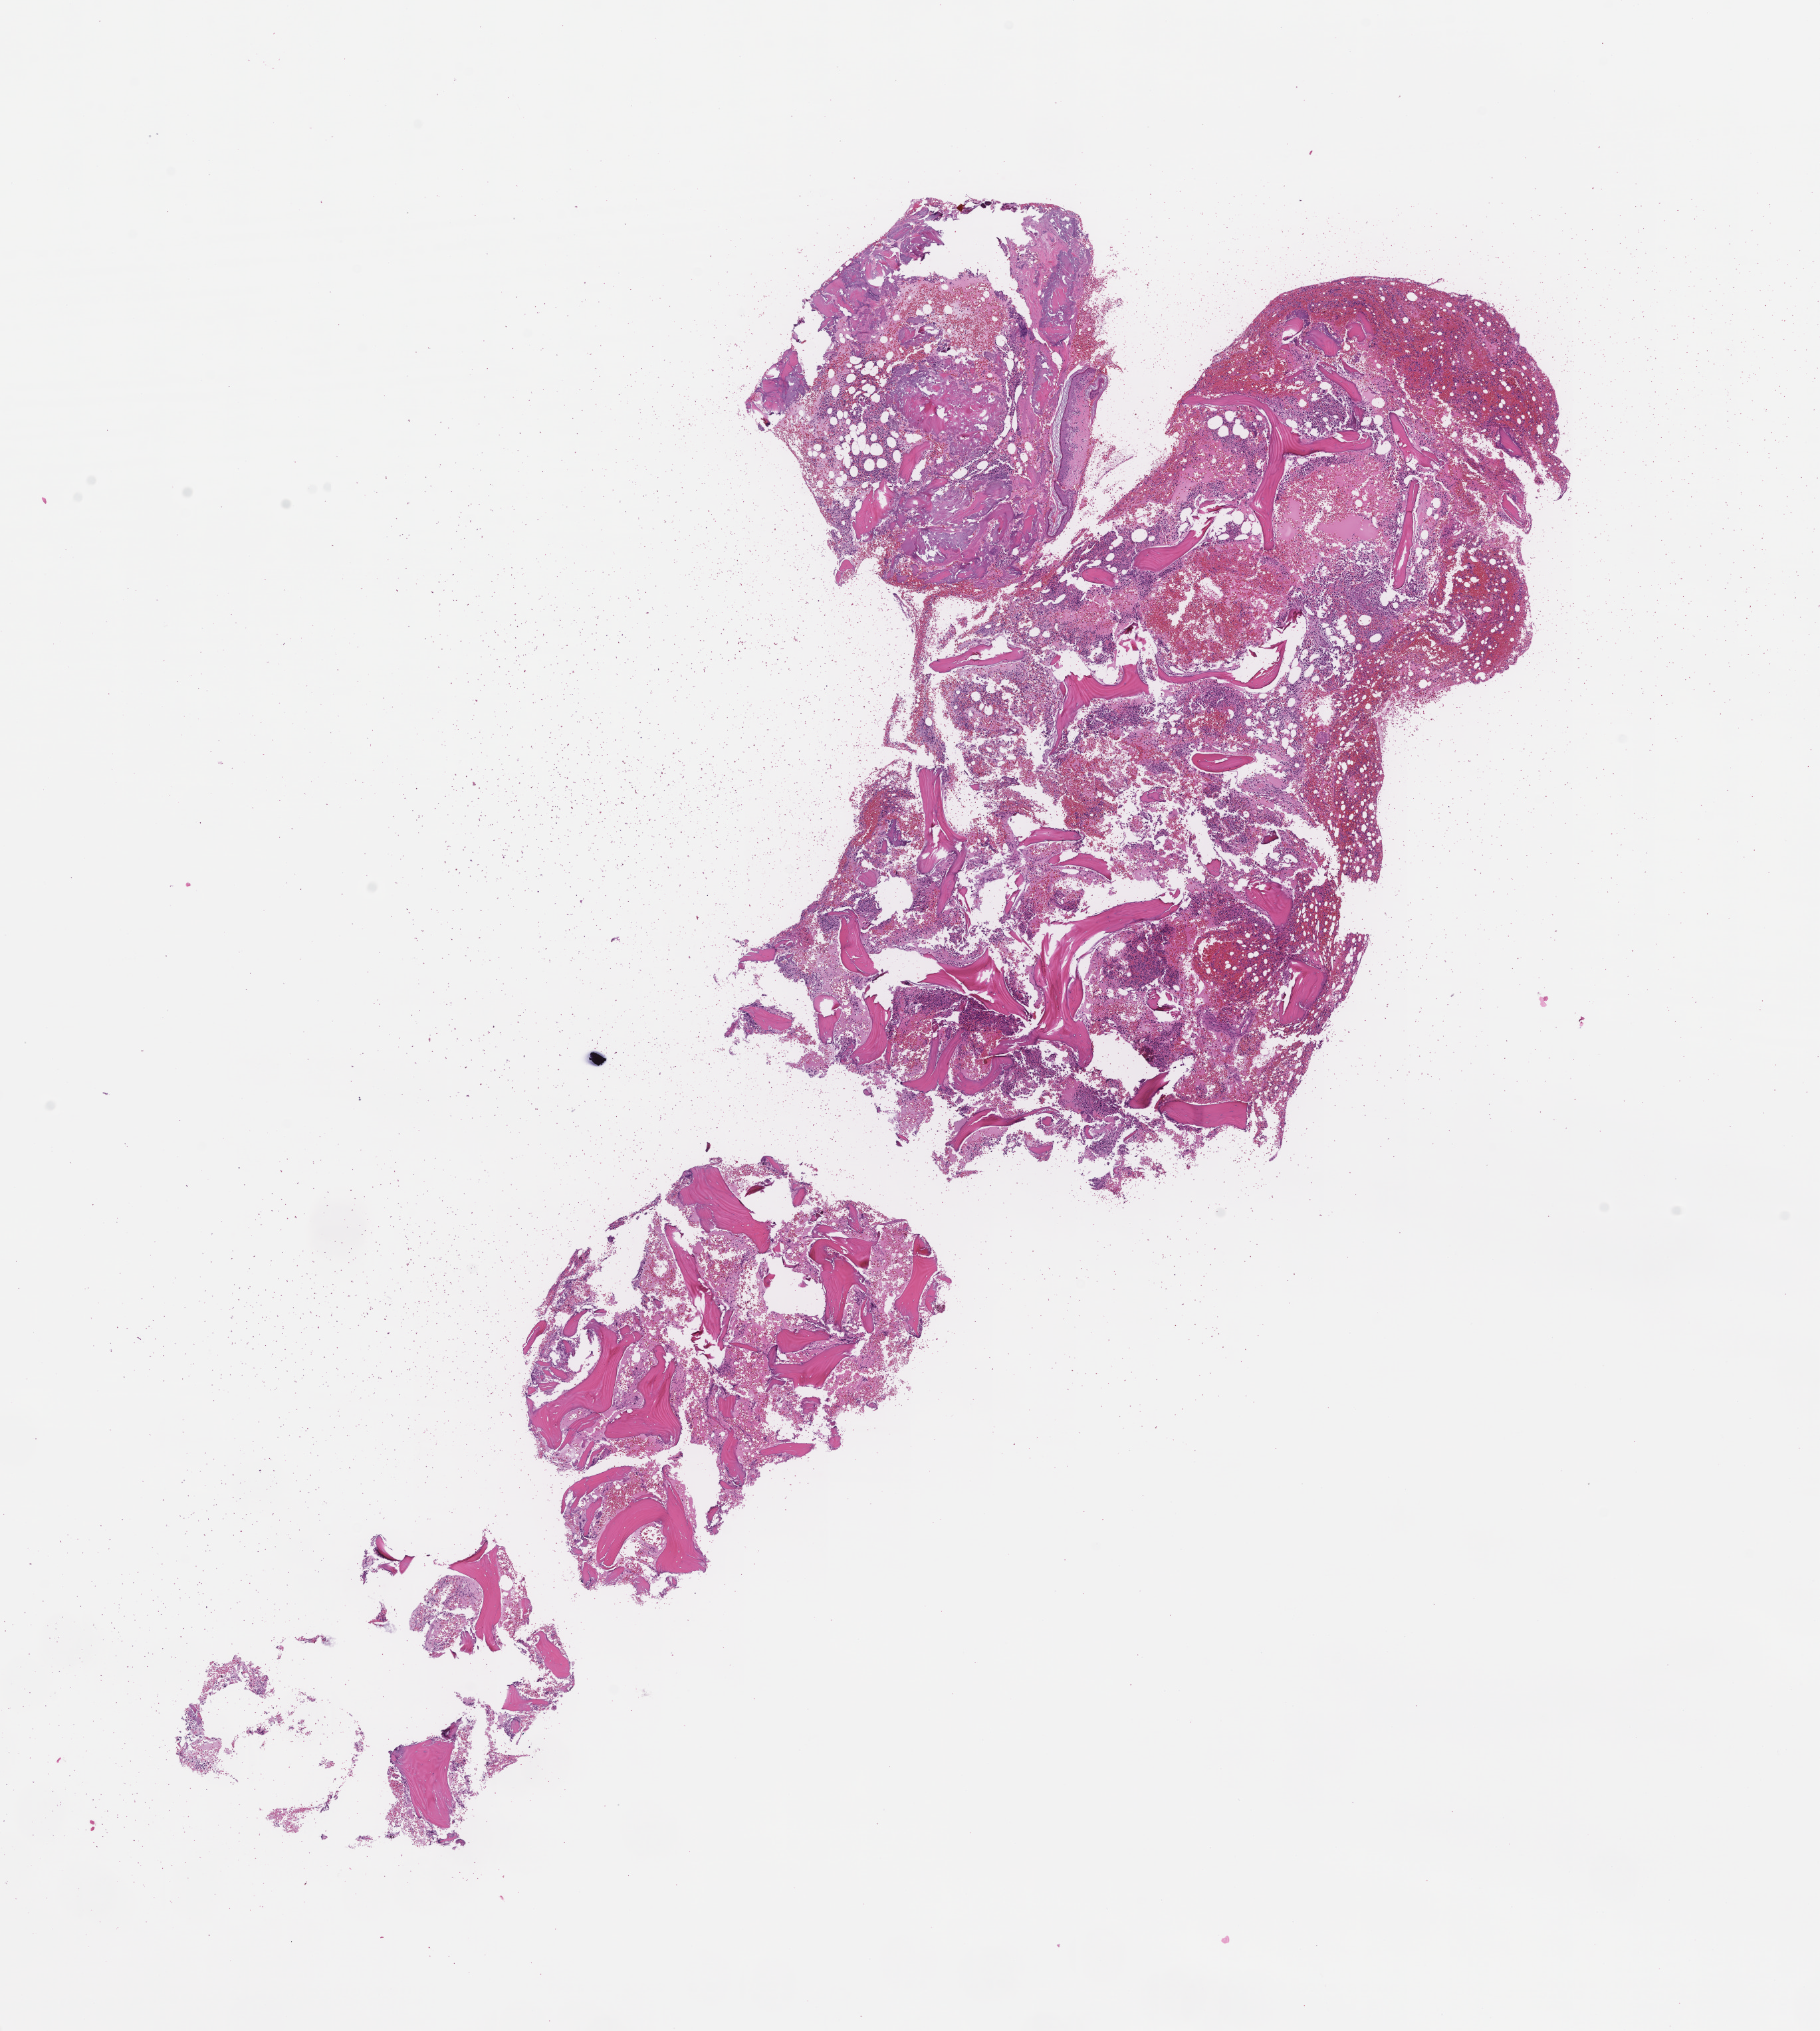
Hematoxylin and eosin (H&E) whole-slide image, whole scanned area (about 11.1 x 12.3 mm) shown as a low-resolution overview; formalin-fixed, paraffin-embedded (FFPE) tissue; site: bone marrow; specimen time point: archival tissue. Patient sex: female.
This section: primary tumor. Diagnosis: Plasma Cell Myeloma.